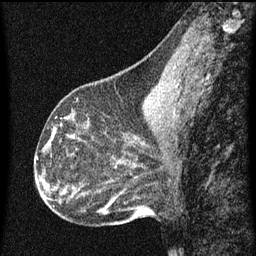
Breast MRI (dynamic contrast-enhanced), one sagittal slice. Position 28 of 60 along the scan axis. Dynamic contrast-enhanced series, image 2 of 3 at this slice position (ordered by acquisition). 1.5 T. TE 4.2 ms, TR 8 ms. 2 mm slice thickness. 256 × 256 image matrix. Patient: female, 43 years.
Structures marked on this image (semi-automatic segmentation, software-assisted and operator-edited):
- analysis volume of interest (the breast-tissue region the enhancement analysis was run in; not a lesion): box from (x=53, y=104) to (x=100, y=151) px
- tumour enhancement mask (voxels above the 70 % enhancement threshold inside the analysis volume of interest): (x=60, y=118)–(x=70, y=137)